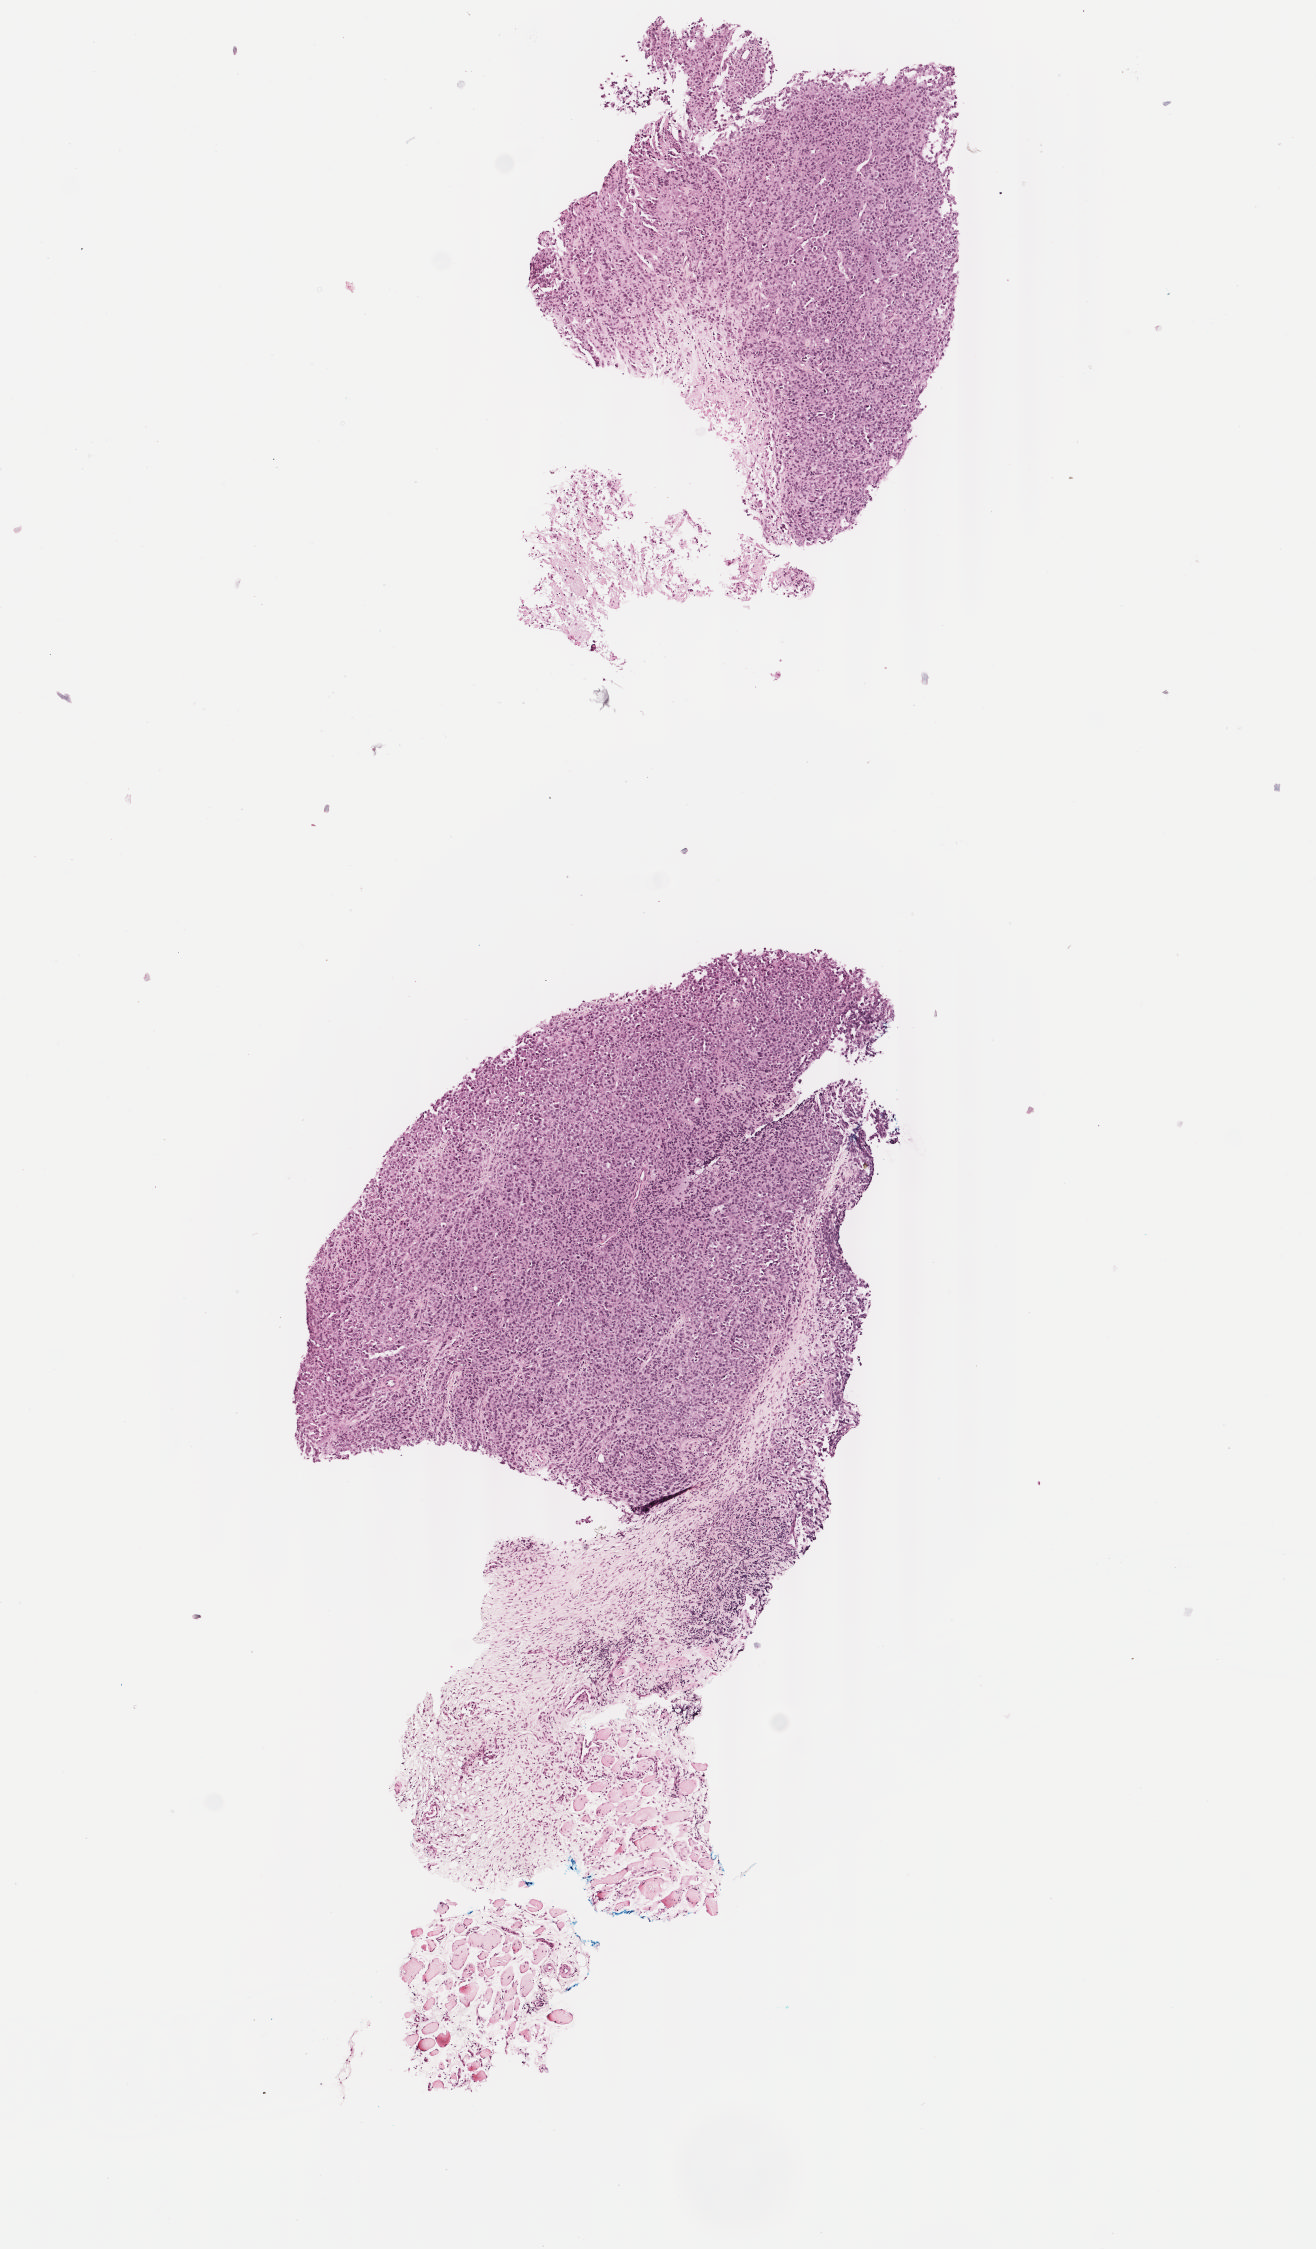
H&E-stained whole-slide image — a low-resolution overview of the entire scanned area, about 5.2 x 8.9 mm (slide scanned at 40x), formalin-fixed paraffin-embedded (FFPE) diagnostic section, skin, primary tumour sample. Male, age 87 years at initial diagnosis.
* diagnosis: Malignant melanoma, NOS
* TNM: TX N0 M1a
* AJCC pathologic stage: IV (7th edition)